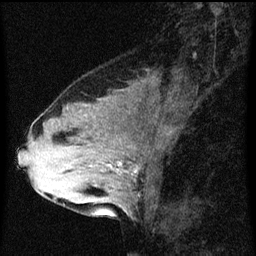
Breast MRI (dynamic contrast-enhanced), one sagittal slice. Slice 27 of 60 in the series (ordered by position). Dynamic contrast-enhanced series, image 2 of 3 at this slice position (ordered by acquisition). 1.5 T. TE 4.2 ms, TR 8 ms. 256 × 256 image matrix. Female patient, age 33 years.
Outlined on this slice (semi-automatic segmentation, software-assisted and operator-edited):
- analysis volume of interest (the breast-tissue region the enhancement analysis was run in; not a lesion): bounding box (x1, y1, x2, y2) in pixels: (61, 126, 145, 213)
- tumour enhancement mask (voxels above the 70 % enhancement threshold inside the analysis volume of interest): (107, 164, 120, 171)